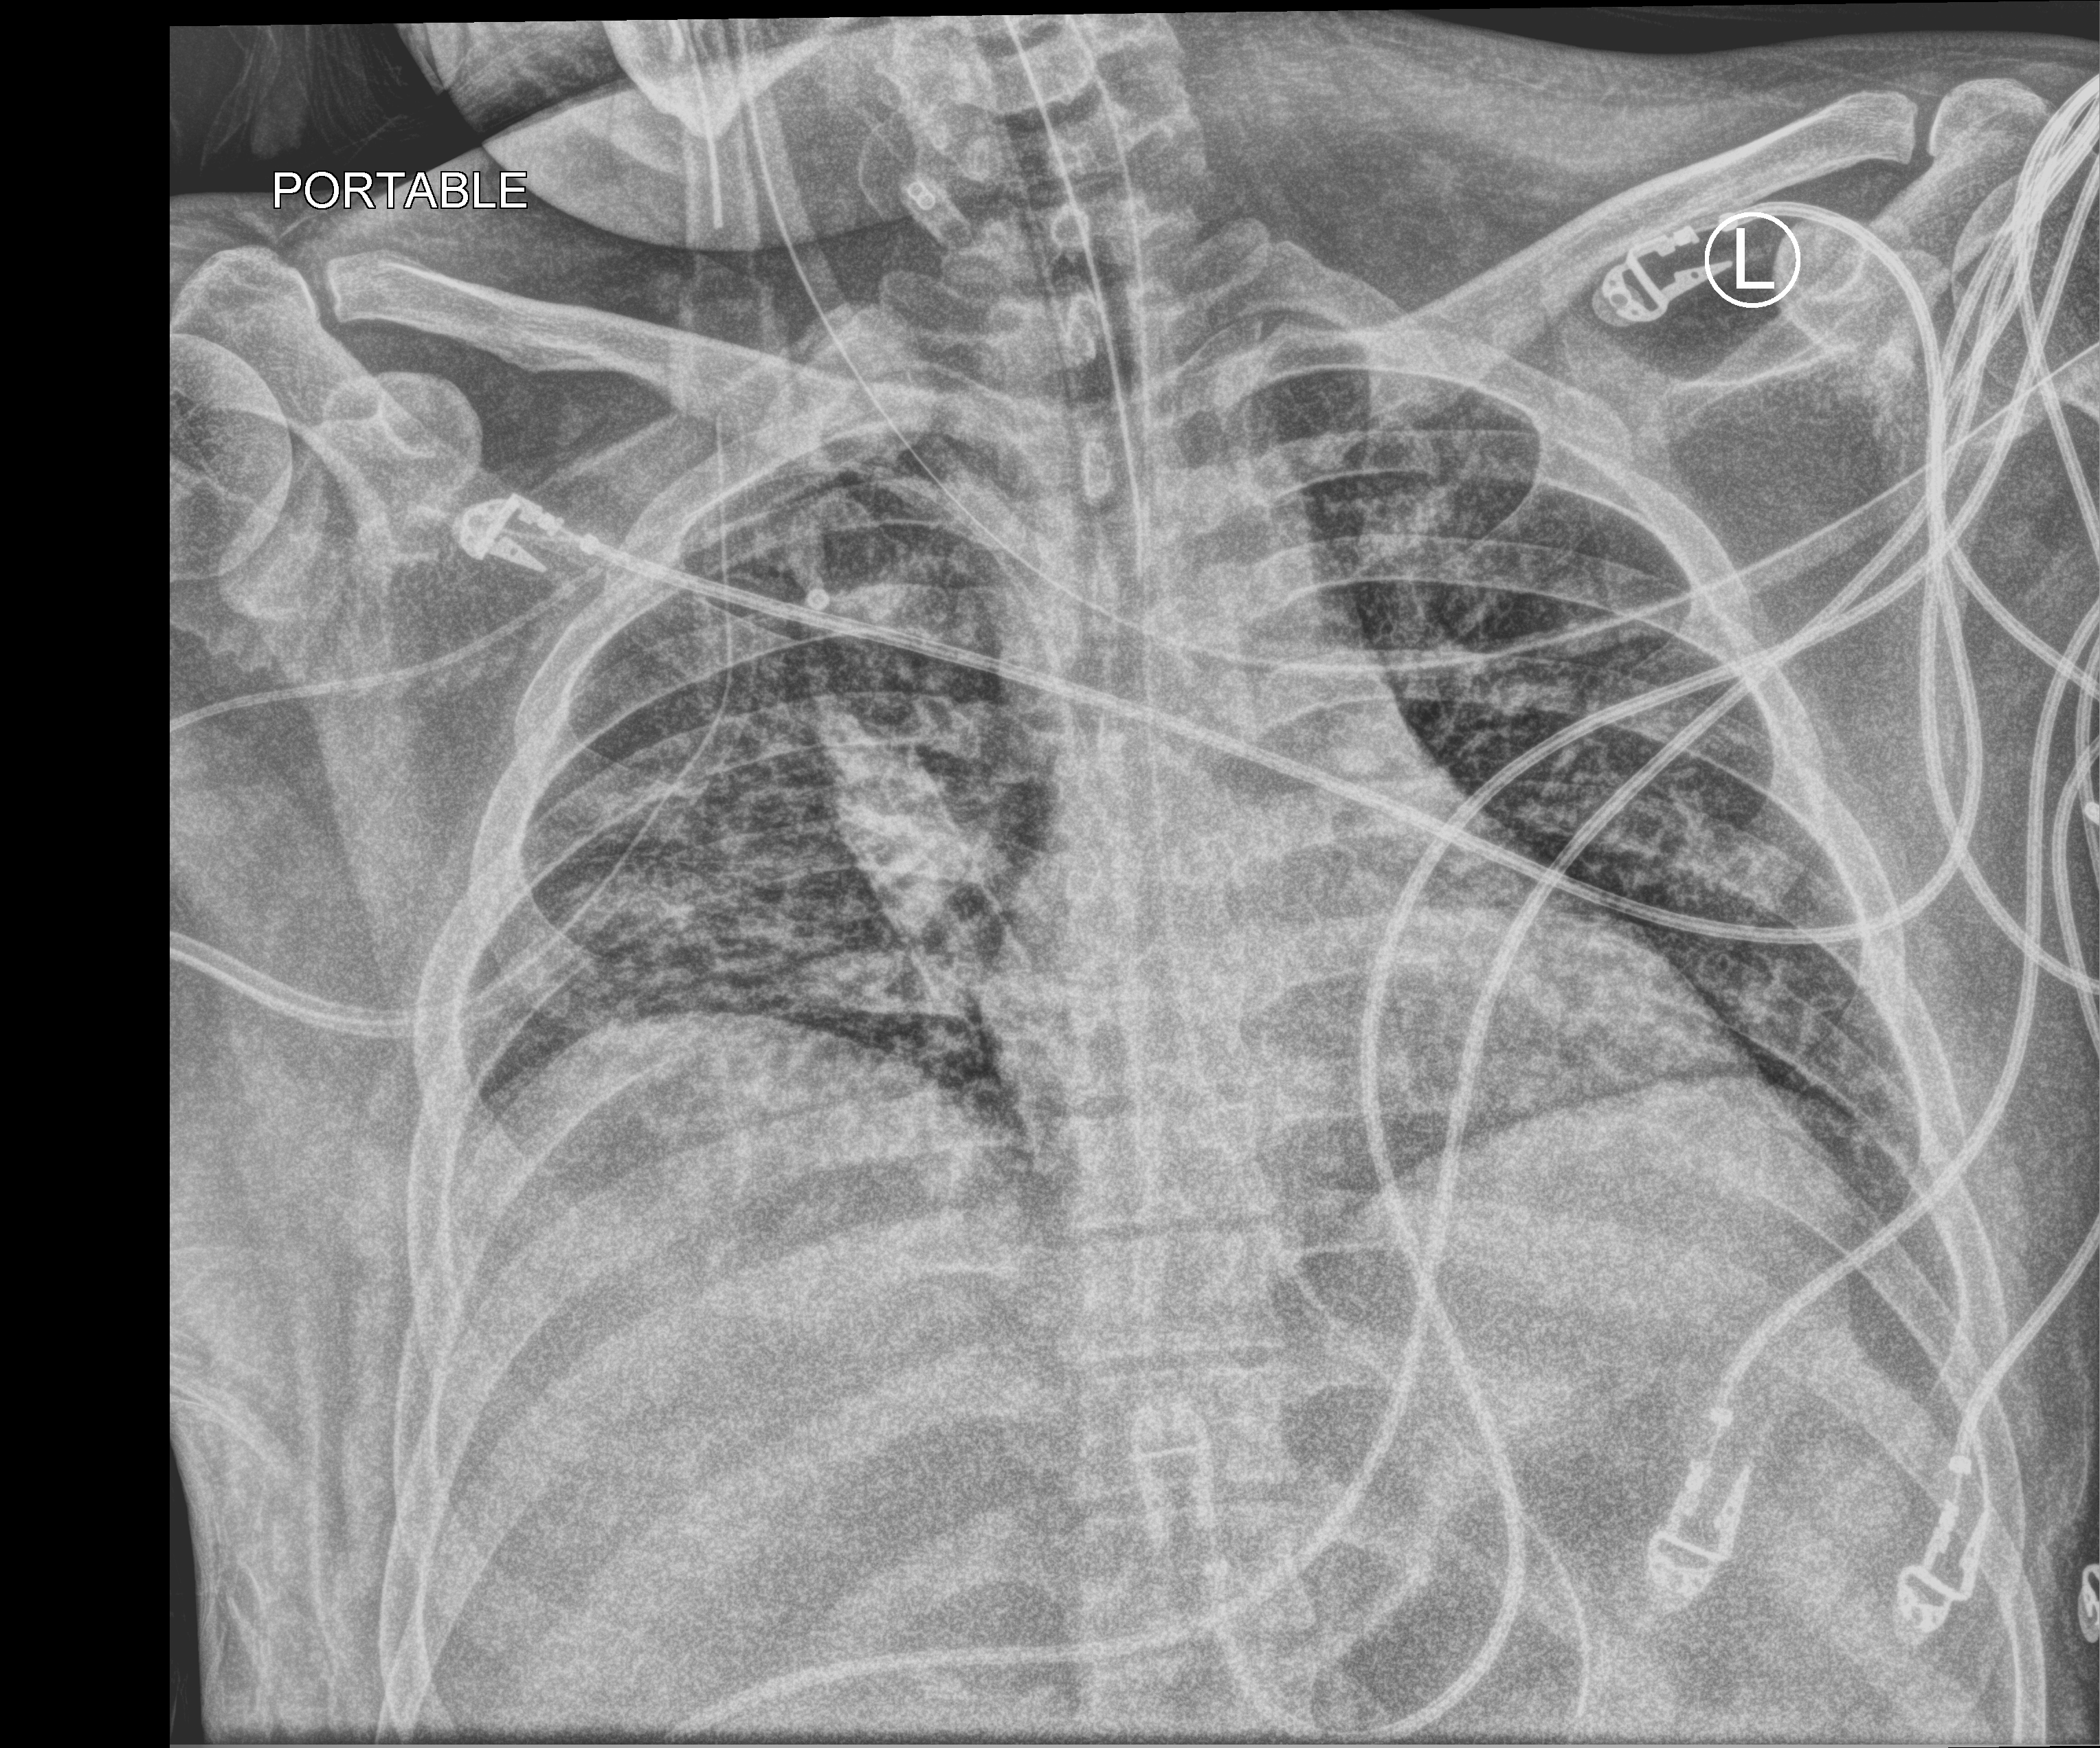
Chest X-ray (portable), anteroposterior (AP) projection. Male patient hospitalised with COVID-19, age 18–59 years.
Admission-level facts for this patient (not findings on this image; timing relative to this image not recorded):
- smoking status (admission record): former
- mechanically ventilated during this hospital stay: yes
- admitted to intensive care during this hospital stay: yes